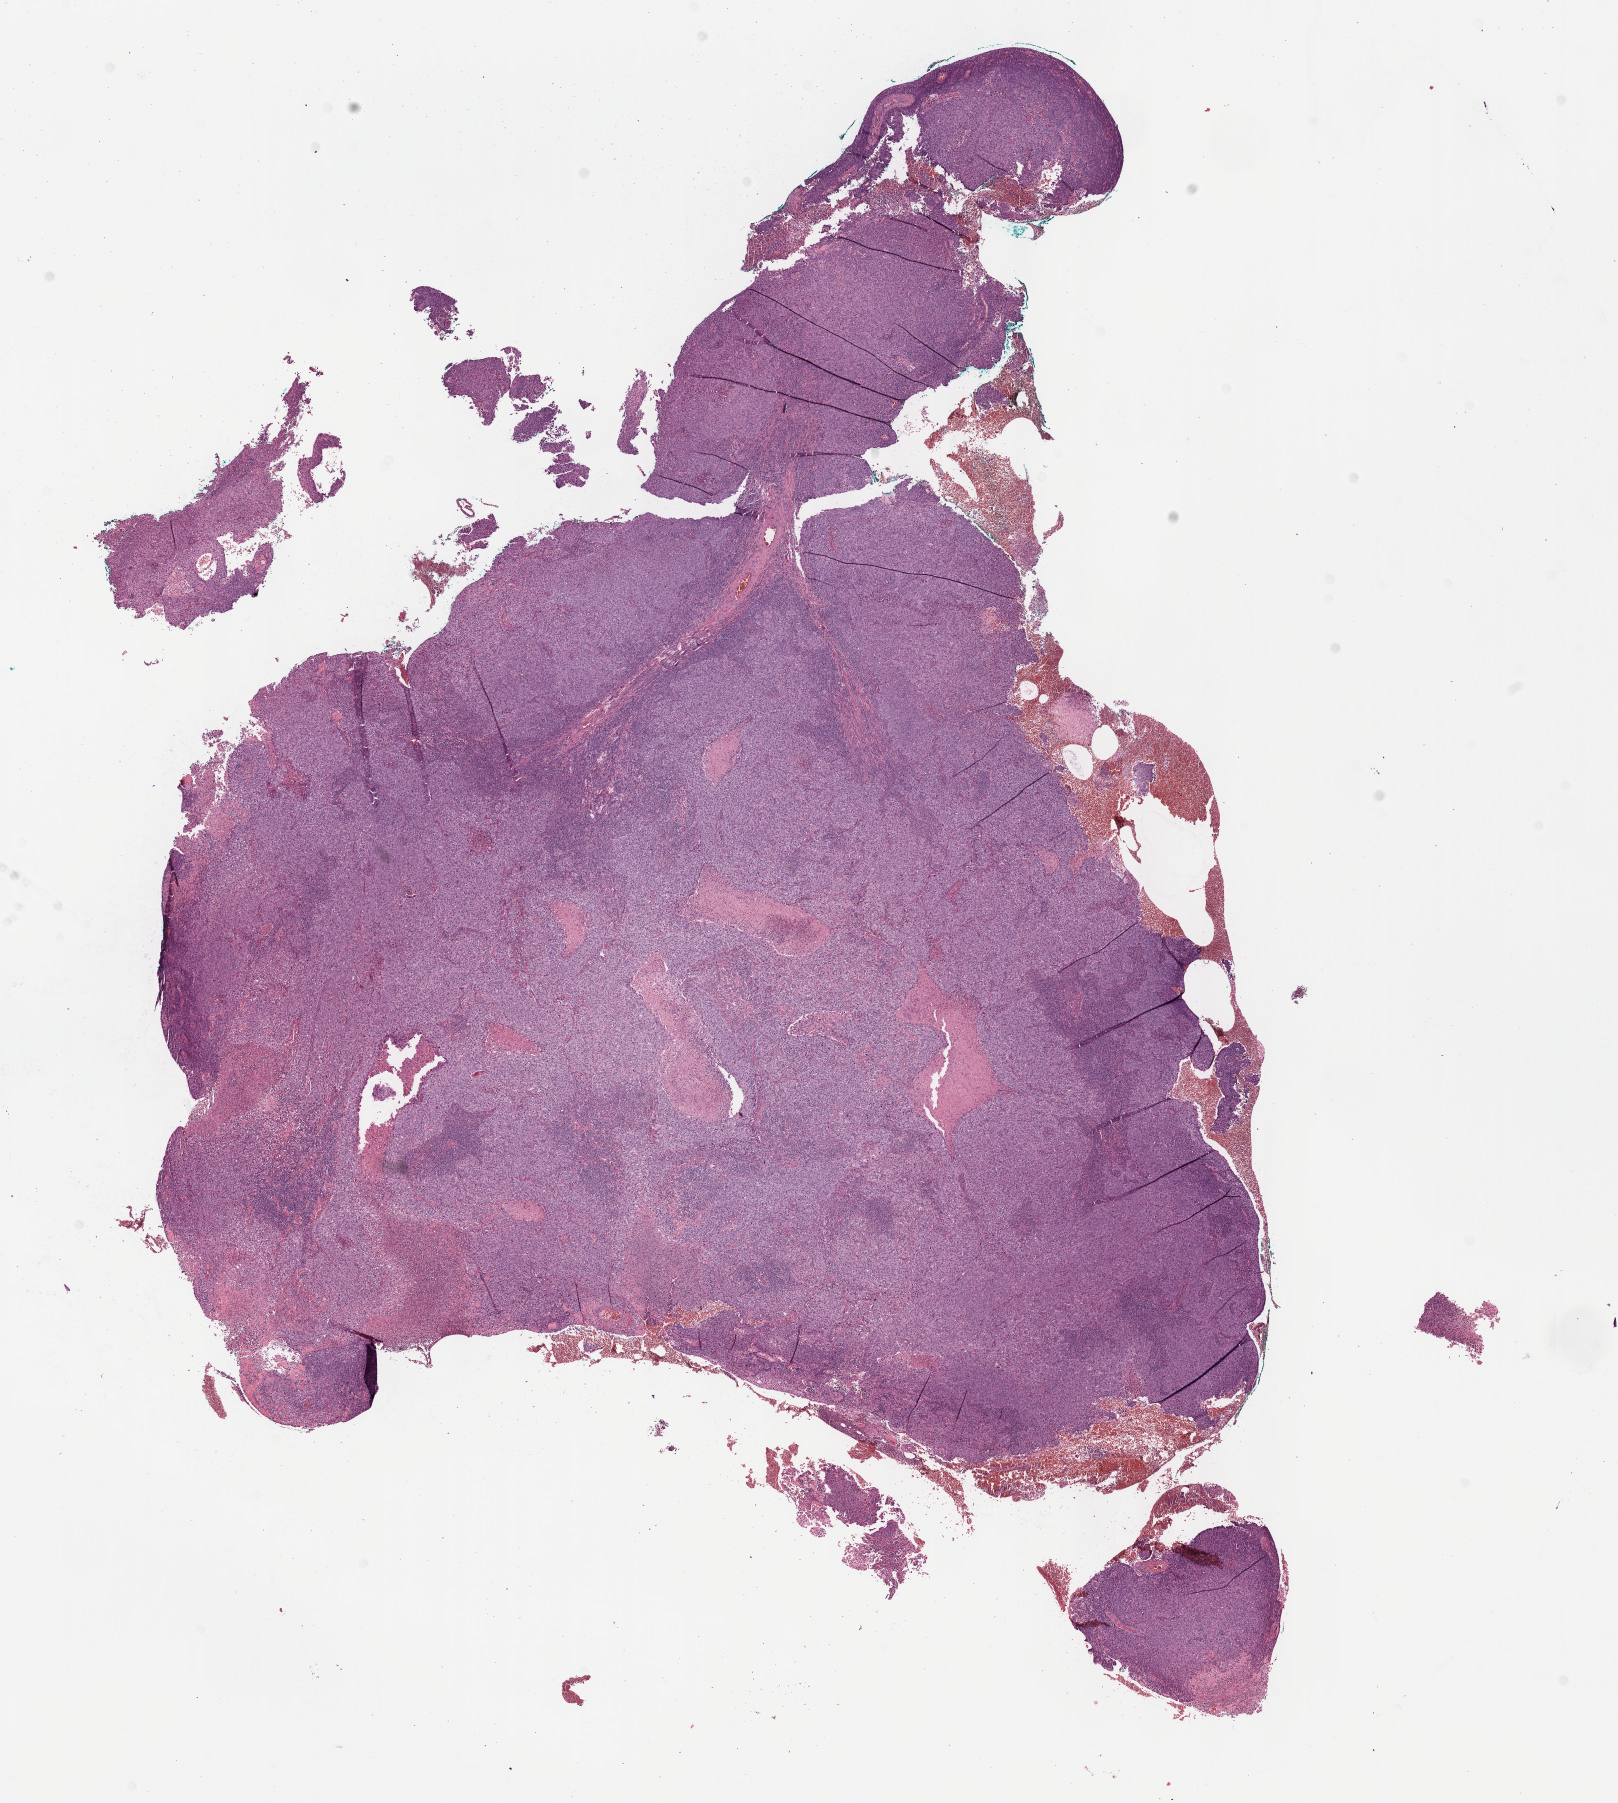
Digitized Hematoxylin and eosin (H&E) stained tissue section (whole slide), shown as a low-resolution overview of the whole scanned area (about 13.1 x 14.6 mm), formalin-fixed paraffin-embedded (FFPE) diagnostic section, primary tumour sample from the cervix. Patient: female, age at initial diagnosis 54 years. Histologic grade: G3 (poorly differentiated).
FIGO stage: IIB. Diagnosis: Squamous cell carcinoma, NOS (cervix uteri). Lymph nodes positive (case pathology): 0 of 51 examined.